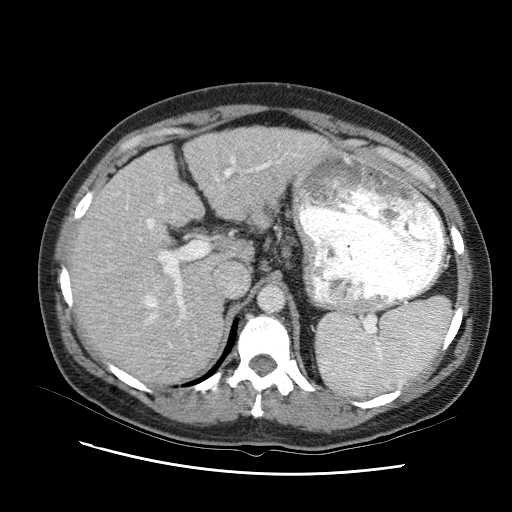
Contrast-enhanced abdominal CT (liver protocol), one axial slice. Position 63 of 95 along the scan axis. Reconstruction kernel STANDARD. One of 2 acquisitions stored at this slice position. Soft-tissue window (W 400 / L 40 HU). 2.5 mm slice thickness. 512 × 512 image matrix, field of view 360 × 360 mm. Case-level facts recorded for this patient, not image findings: diagnosis: hepatocellular carcinoma (patient treated with transarterial chemoembolisation; whether this scan precedes or follows treatment is not stated here); TNM stage (as recorded): Stage-I; Child-Pugh class: B; tumour differentiation: moderately differentiated; tumour nodularity: uninodular.
Structures marked on this image (semi-automatically segmented with operator editing):
- abdominal aorta: box from (x=257, y=284) to (x=283, y=311) px
- liver parenchyma outside the tumour (the mass and vessels are separate outlines, so this box may not span the whole liver): (x=68, y=124)–(x=332, y=372)
- liver vessels: (x=93, y=155)–(x=286, y=349)